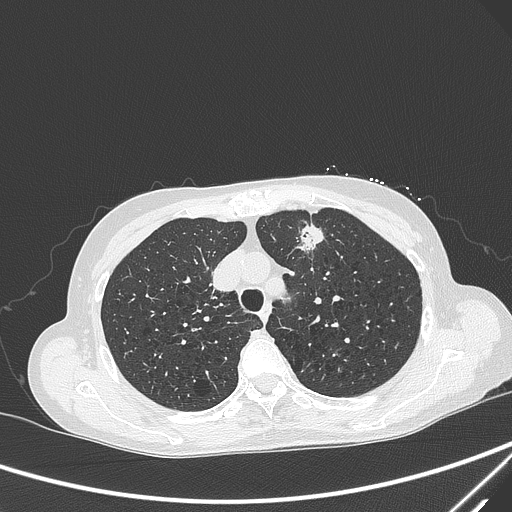
Chest CT, one axial slice. Position 230 of 299 along the scan axis. 120 kVp. Lung window (W 1500 / L -600 HU). 1 mm slice thickness. 512 × 512 image matrix. Patient: female, 71 years. From the clinical record (not read from this slice): clinical TNM (as recorded): T1c N0 M0; histopathological grade: G2-3.
Annotated regions visible in this slice (bounding box drawn by a radiologist):
- lung tumour (recorded histology: adenocarcinoma): bounding box <294,218,329,260> (left, top, right, bottom; pixels)